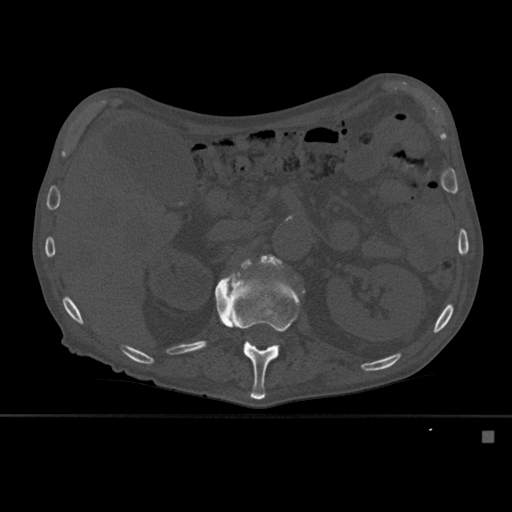
CT including the spine, one axial slice; position 252 of 527 along the scan axis; bone window (W 1800 / L 400 HU); 1.5 mm slice thickness; 512 × 512 image matrix, field of view 373 × 373 mm. Male patient, age 78 years. From the clinical record (not read from this slice): primary cancer: prostate.
Annotated regions visible in this slice (semi-automatically segmented with operator editing):
- L1 vertebra: bounding box (x1, y1, x2, y2) in pixels: (215, 272, 300, 400)
- L2 vertebra: (241, 254, 284, 270)